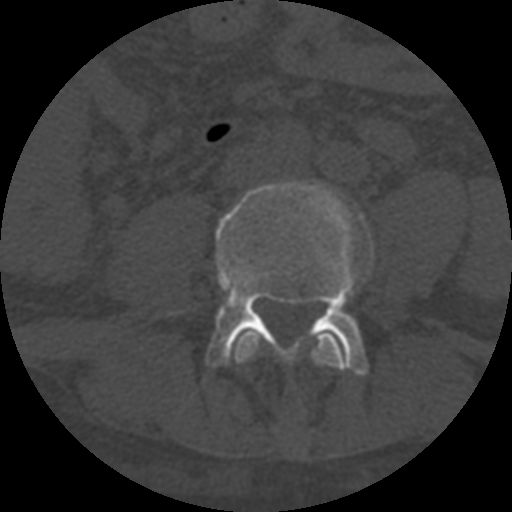
CT including the spine, one axial slice; slice 216 of 708 in the series (ordered by position); reconstruction kernel STANDARD; 120 kVp; one of 3 acquisitions stored at this slice position; bone window (W 1800 / L 400 HU); 1.25 mm slice thickness; 512 × 512 image matrix, field of view 160 × 160 mm. Patient age 55 years. From the clinical record (not read from this slice): primary cancer: colon.
Annotated regions visible in this slice (semi-automatic segmentation, software-assisted and operator-edited):
- L3 vertebra: box from (x=233, y=330) to (x=347, y=371) px
- L4 vertebra: (x=162, y=180)–(x=374, y=375)